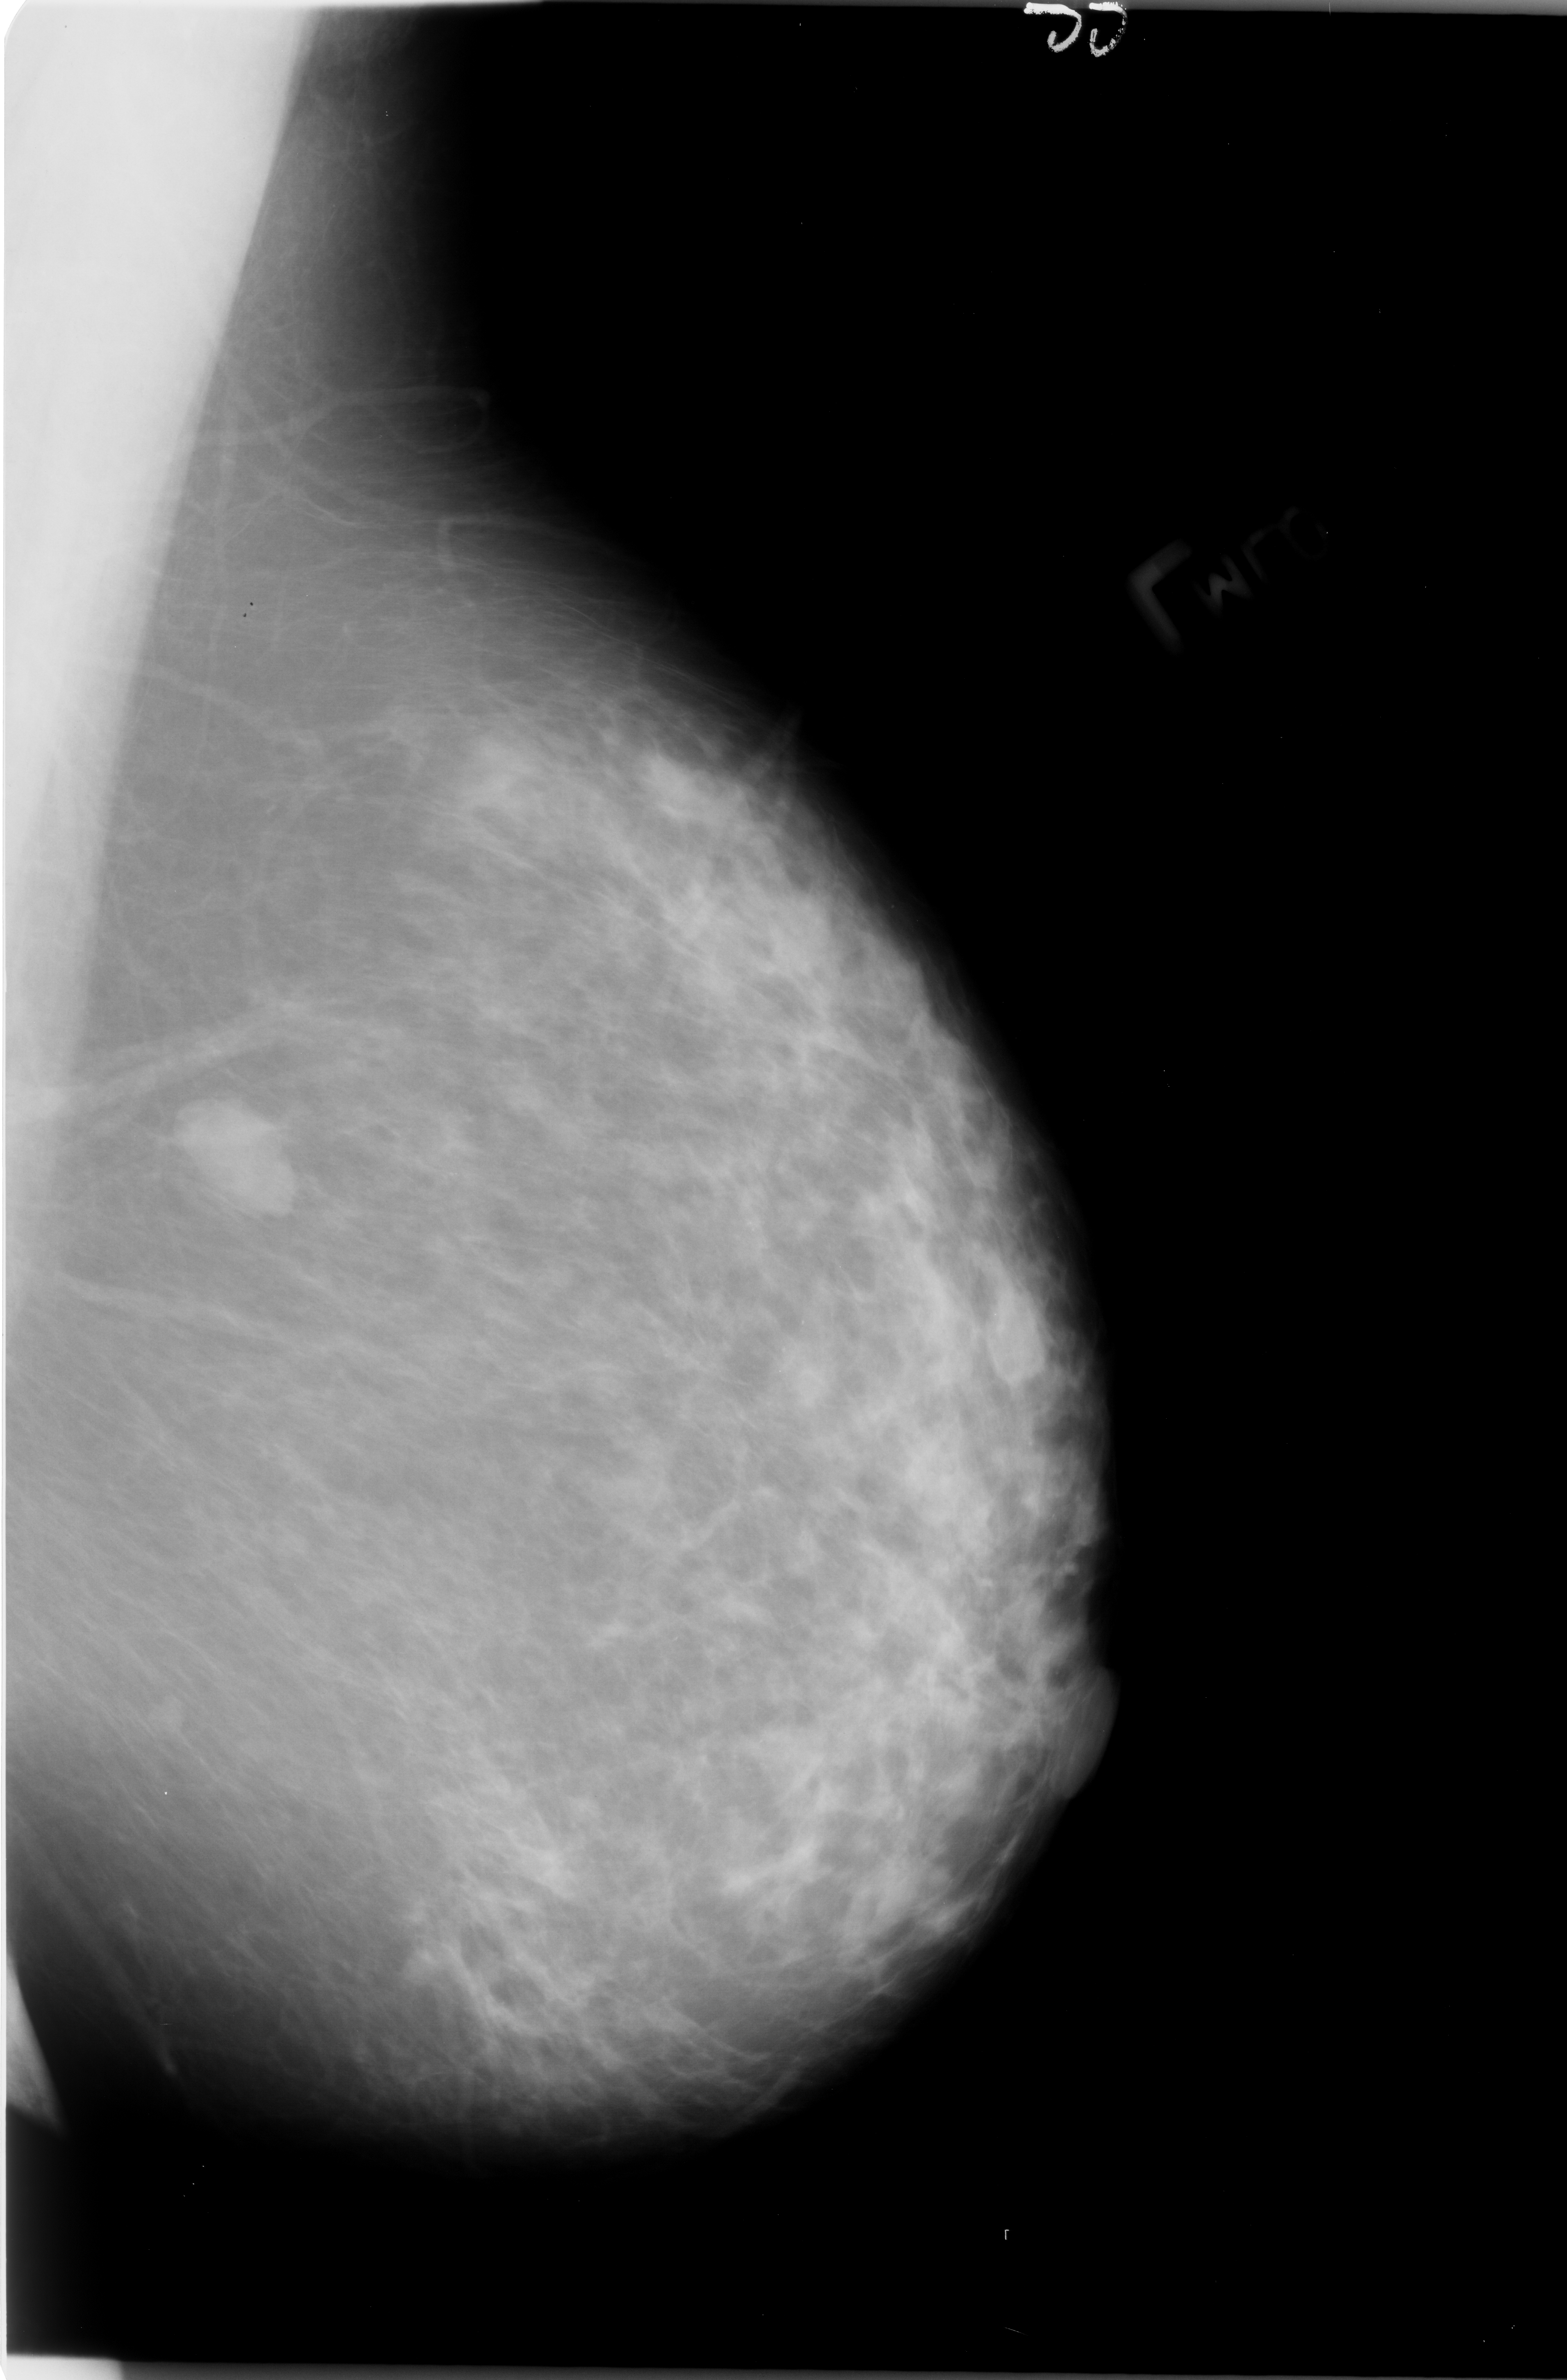
Digitized screen-film mammogram; left breast; MLO view; breast composition: scattered fibroglandular densities (BI-RADS density category 2 of 4); 1567 × 2380 image matrix.
Marked abnormalities (boxes around the expert regions of interest):
- mass, shape lobulated / oval, margins circumscribed; BI-RADS assessment category 4; pathology result (as recorded, not read from the image): benign: bounding box <153,1089,306,1224> (left, top, right, bottom; pixels)